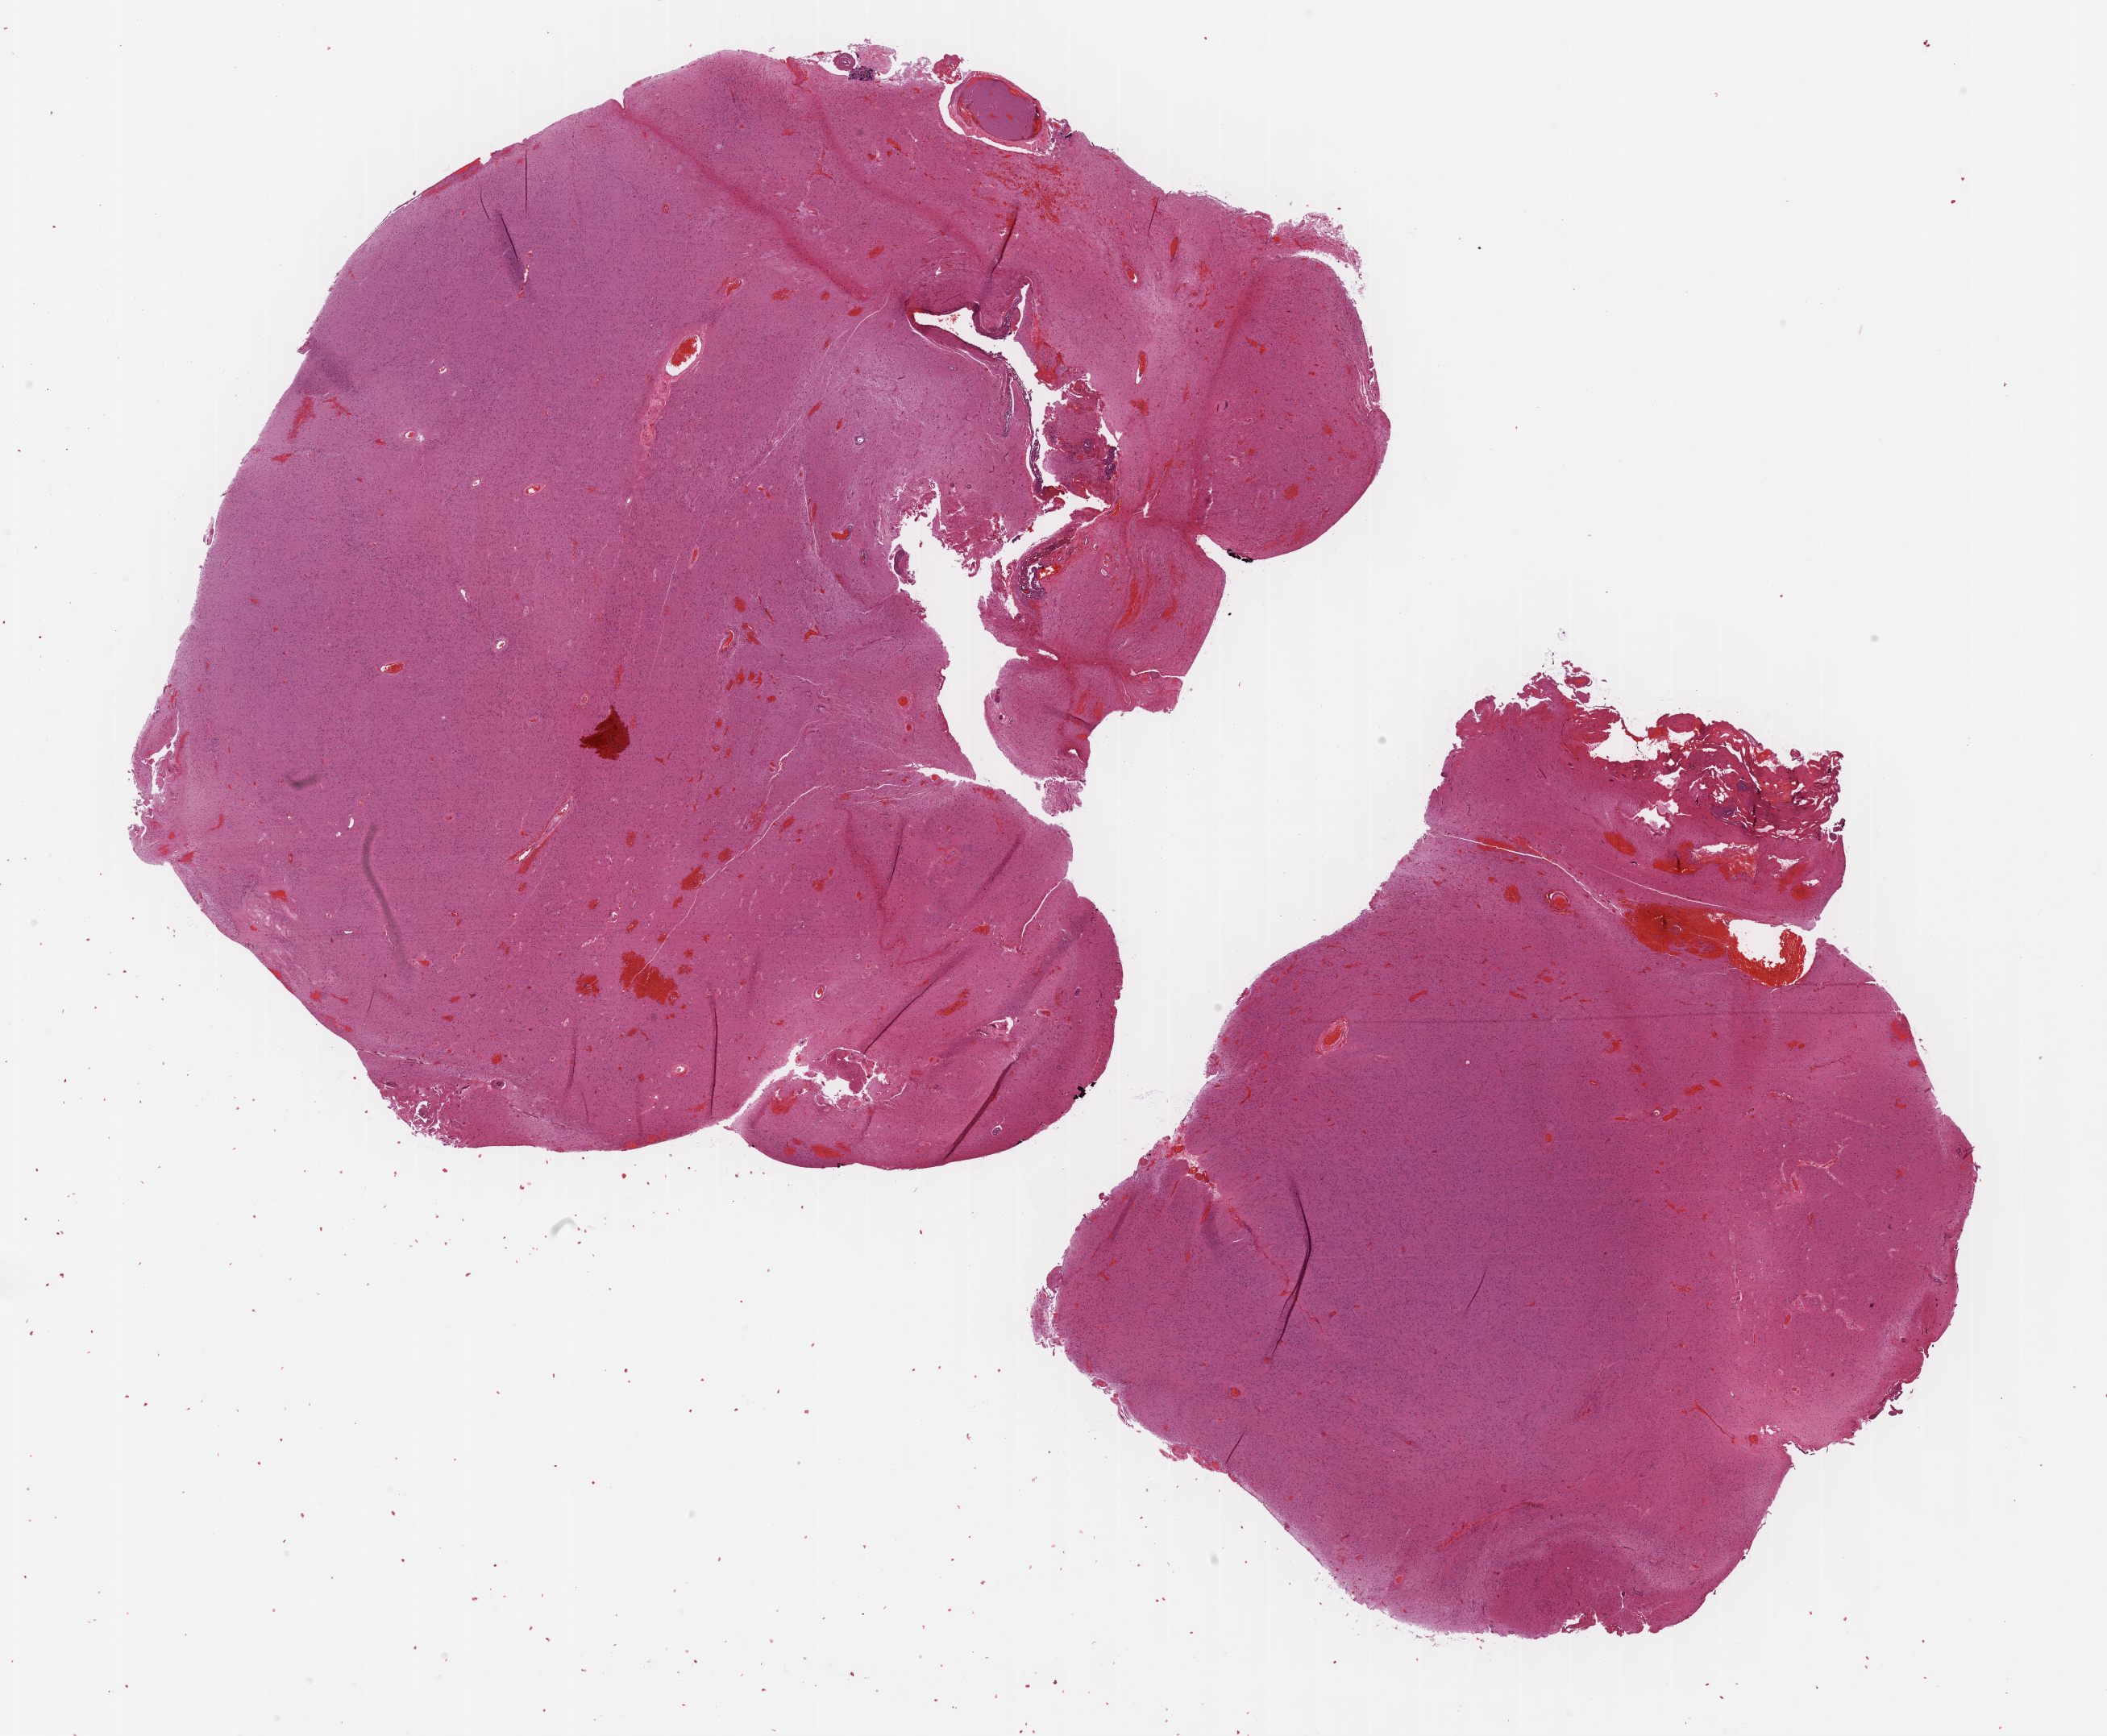
Whole-slide histology image, H&E, shown as a low-resolution overview of the whole scanned area (about 21.1 x 17.4 mm, acquisition: 40x scan), formalin-fixed paraffin-embedded (FFPE) diagnostic section, primary tumour sample from the brain. Female, age 32 years at initial diagnosis. Histologic grade: G2 (moderately differentiated).
* diagnosis: Astrocytoma, NOS